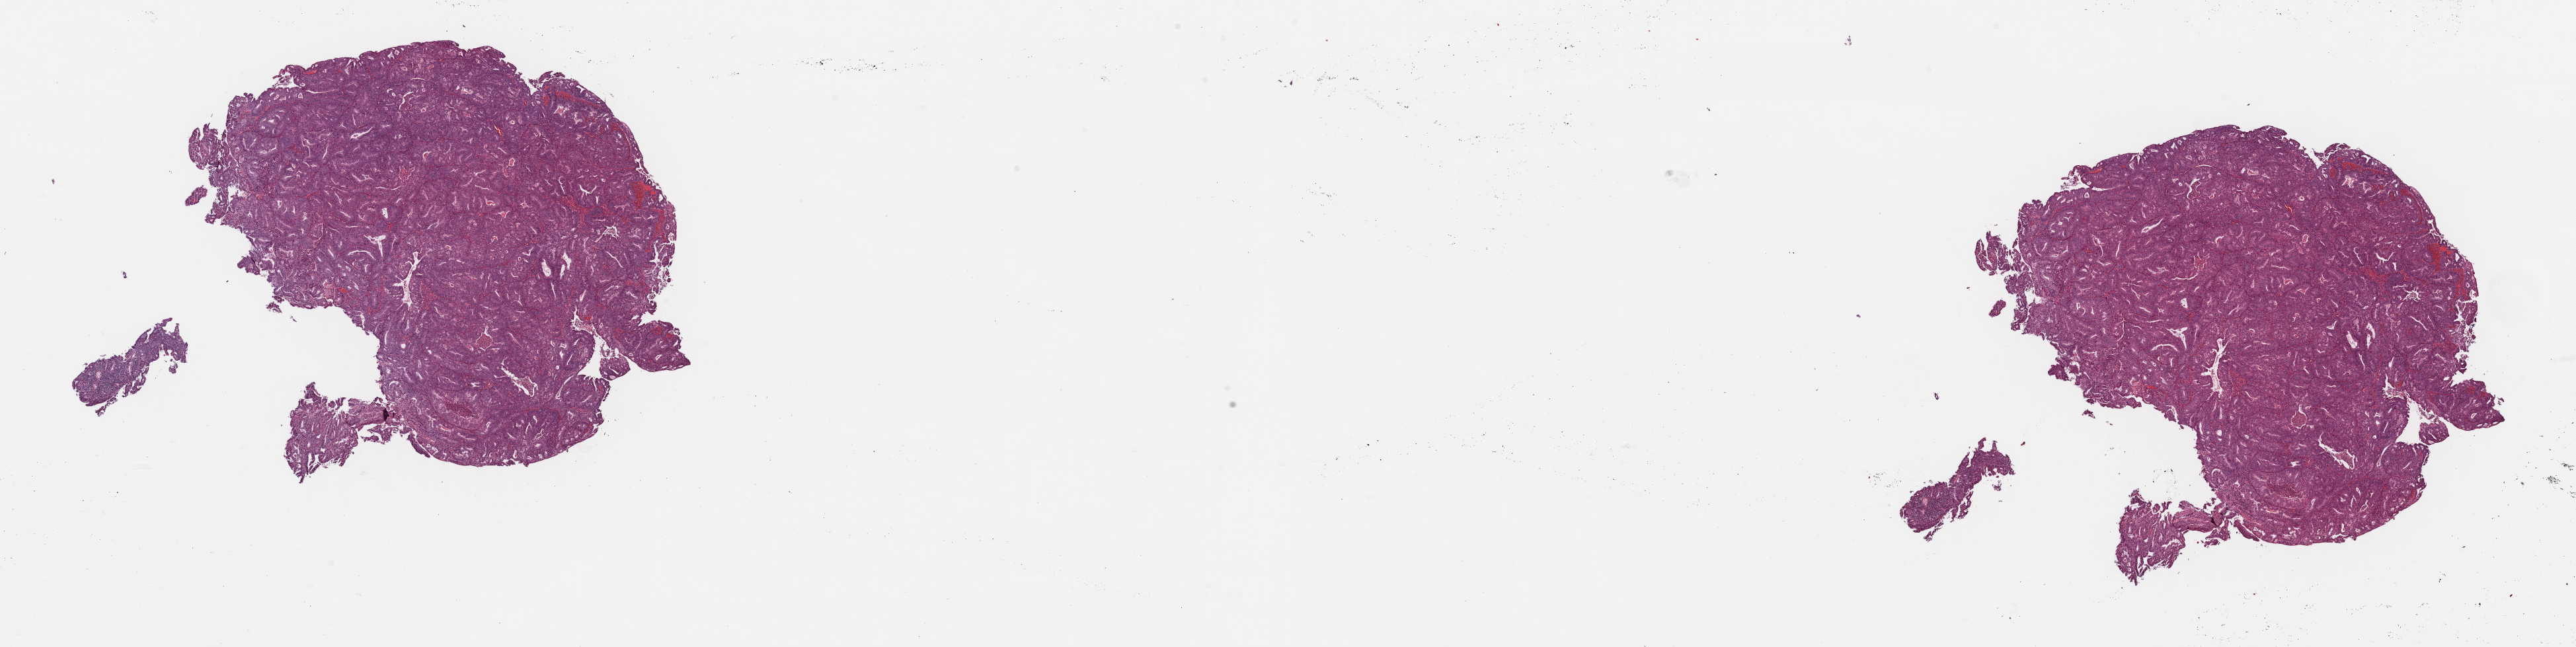
Digitized Hematoxylin and eosin (H&E) stained tissue section (whole slide), low-resolution overview of the scanned area, about 30.7 x 7.7 mm (from a 40x scan). Formalin-fixed paraffin-embedded (FFPE) diagnostic section. Uterus, primary tumour sample. Female patient; age at initial diagnosis 57 years.
Diagnosis: Endometrioid adenocarcinoma, NOS (endometrium).